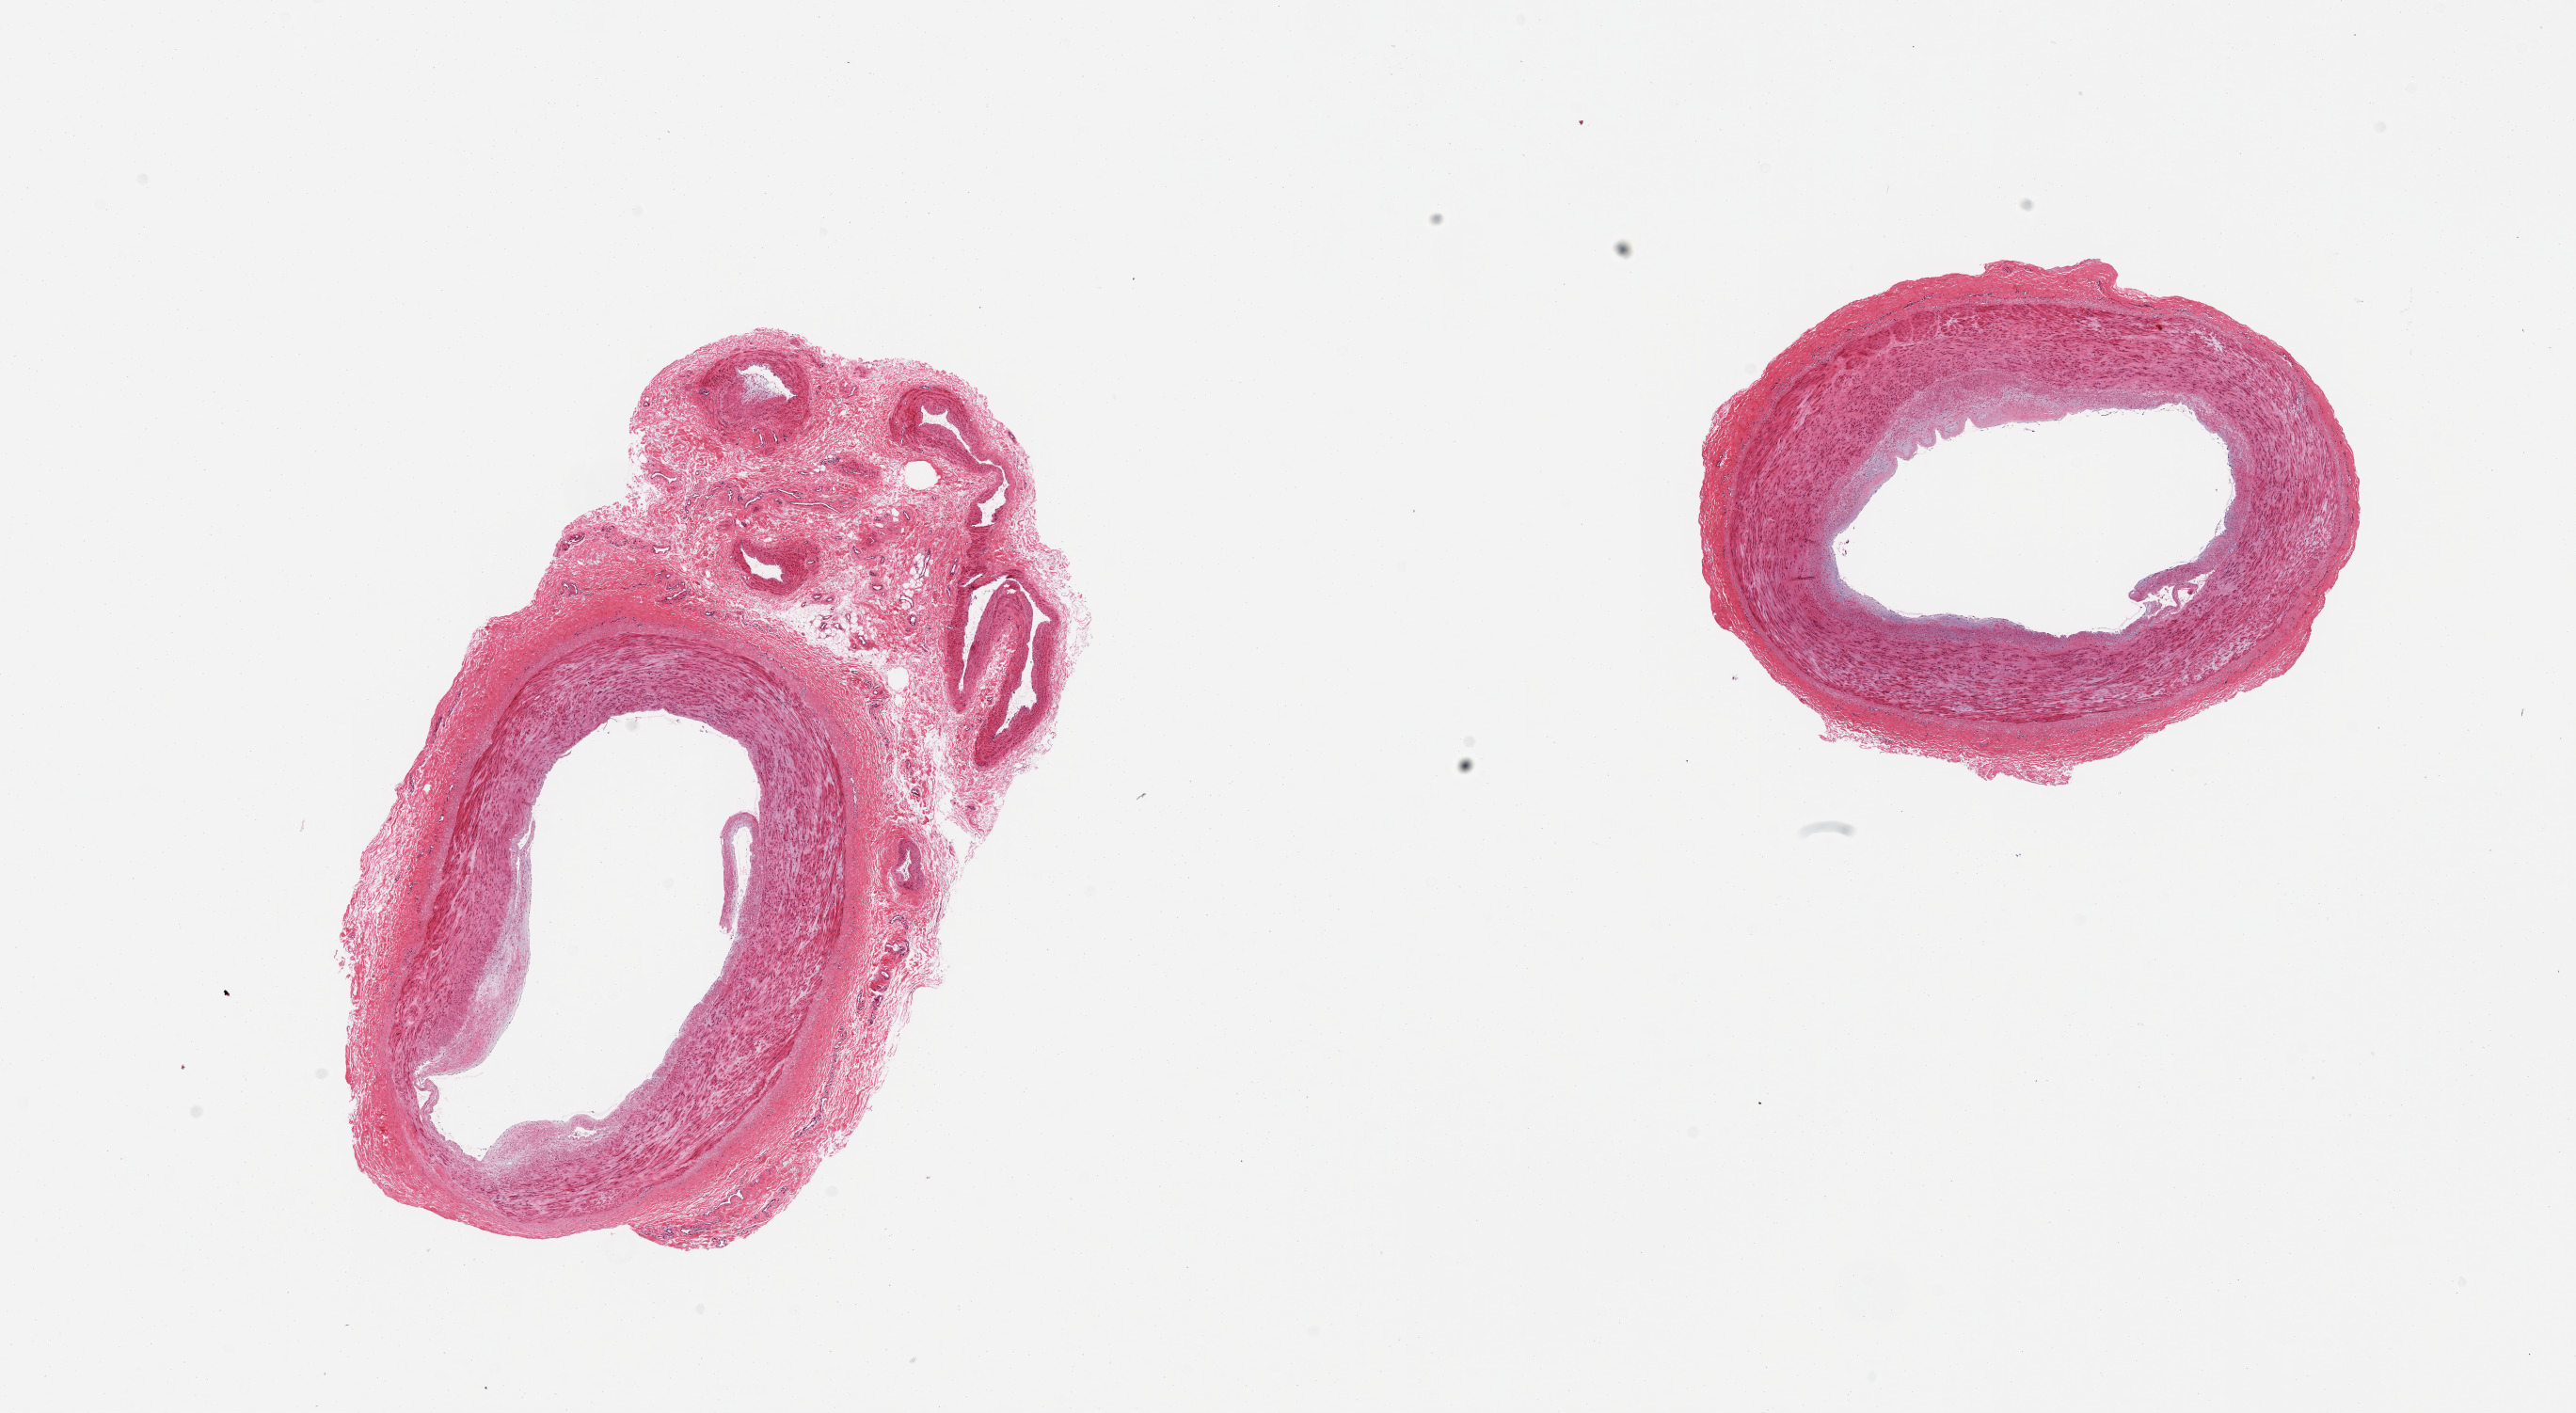
Digitized haematoxylin and eosin-stained section, whole scanned area (about 21.7 x 11.9 mm, from a 20x scan) shown as a low-resolution overview, PAXgene-fixed paraffin-embedded (PFPE) section, section of tibial artery (target tissue), tissue donor sample.
Review note (as recorded): 2 pieces, early atheromatous plaque, attachment of fibrofatty tissue/vessels.